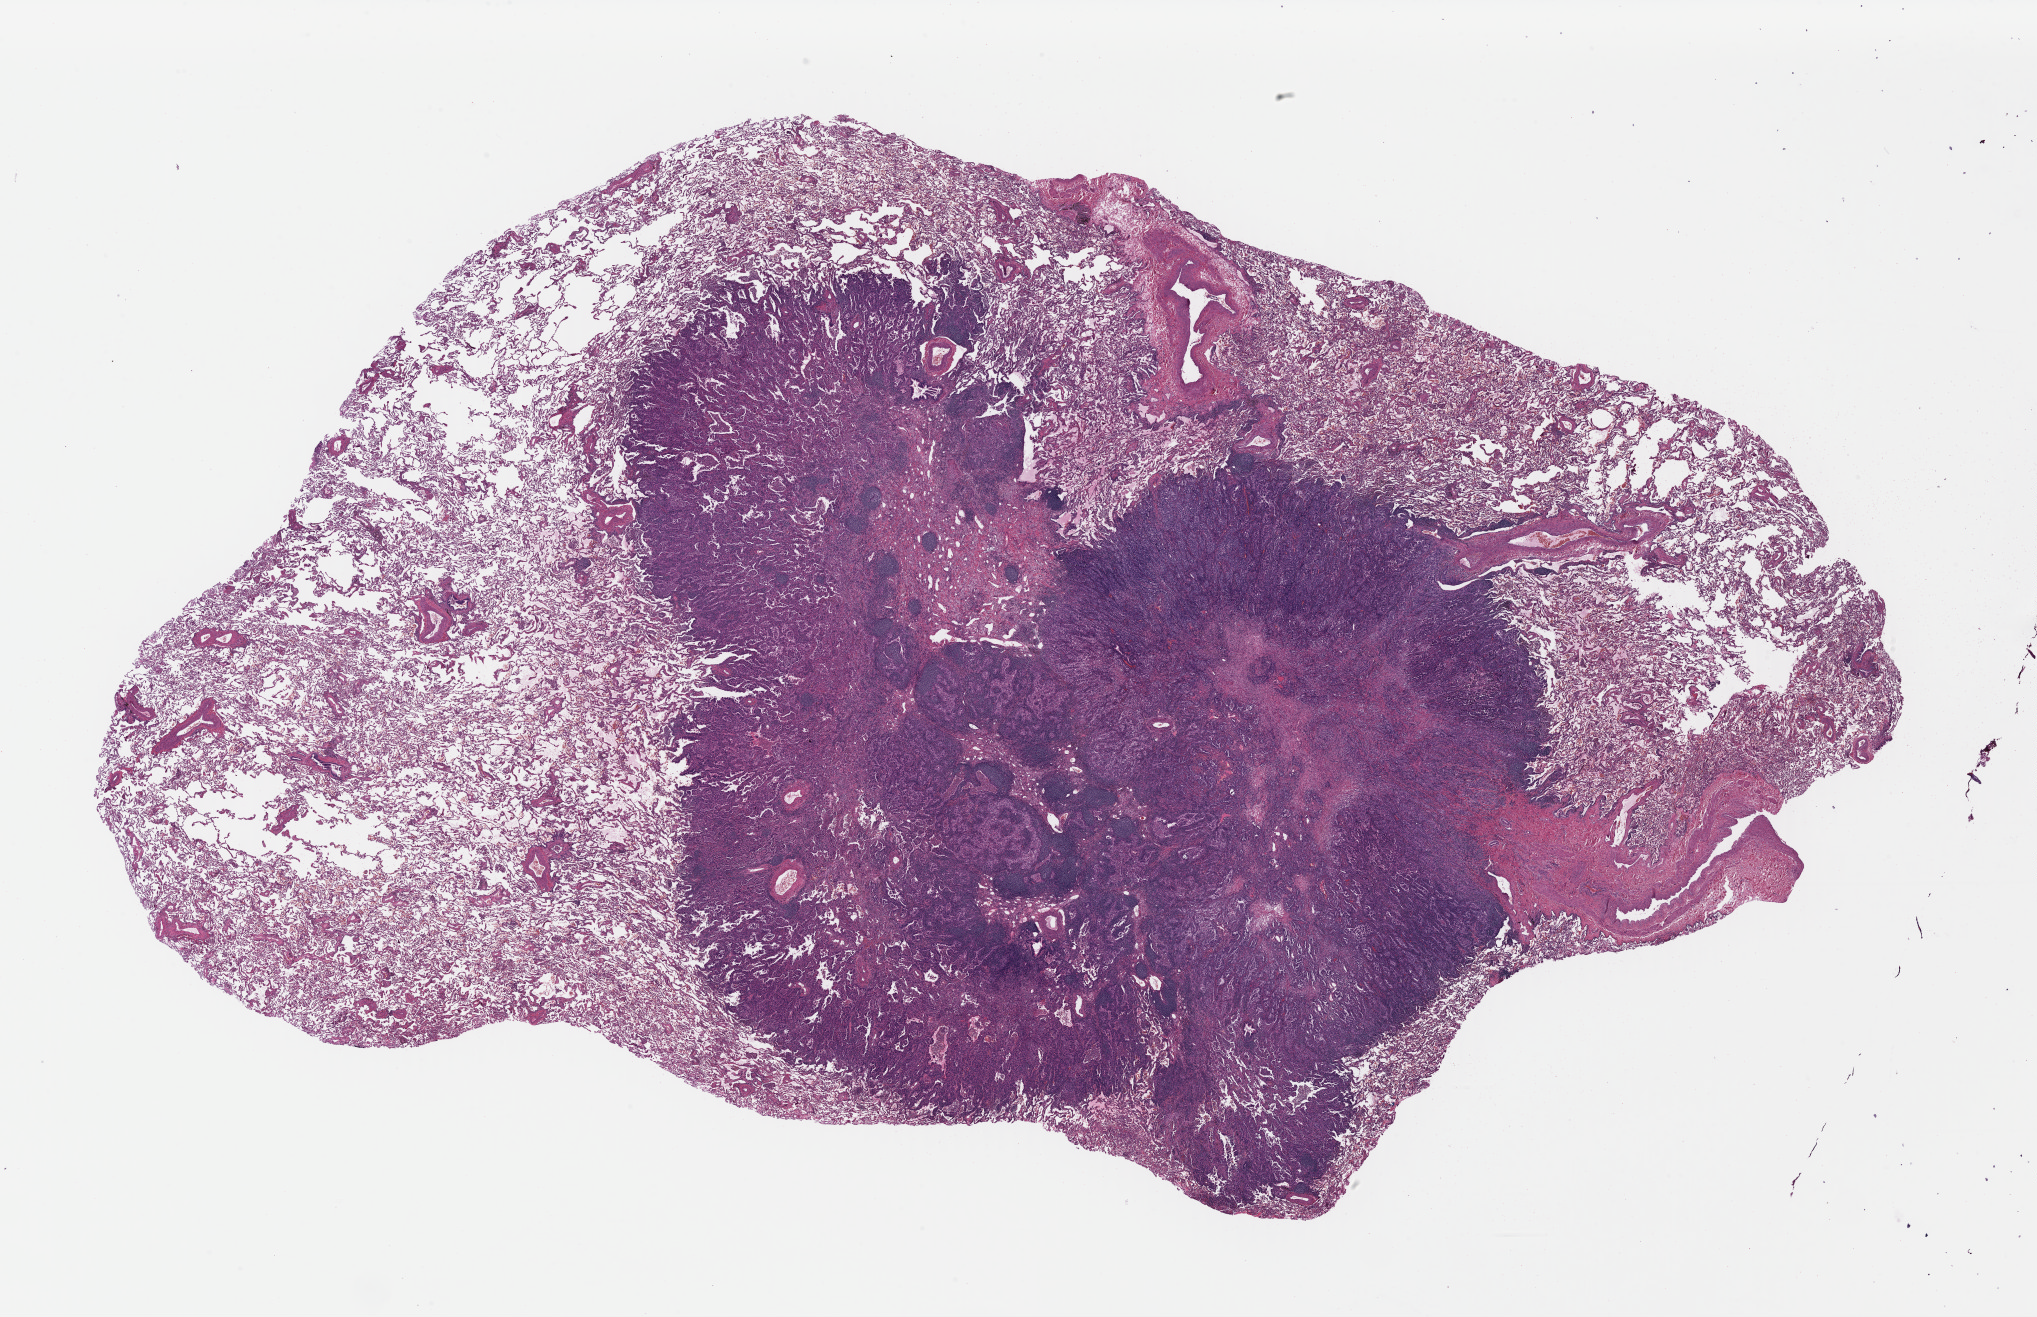
H&E-stained whole-slide image, low-resolution overview of the scanned area, about 32.0 x 20.7 mm; formalin-fixed paraffin-embedded (FFPE) diagnostic section; sample: primary tumour, lung. Female, age 60 years at initial diagnosis.
* pathologic diagnosis: Adenocarcinoma, NOS (upper lobe, lung)
* AJCC pathologic stage: IA (7th edition)
* laterality: right